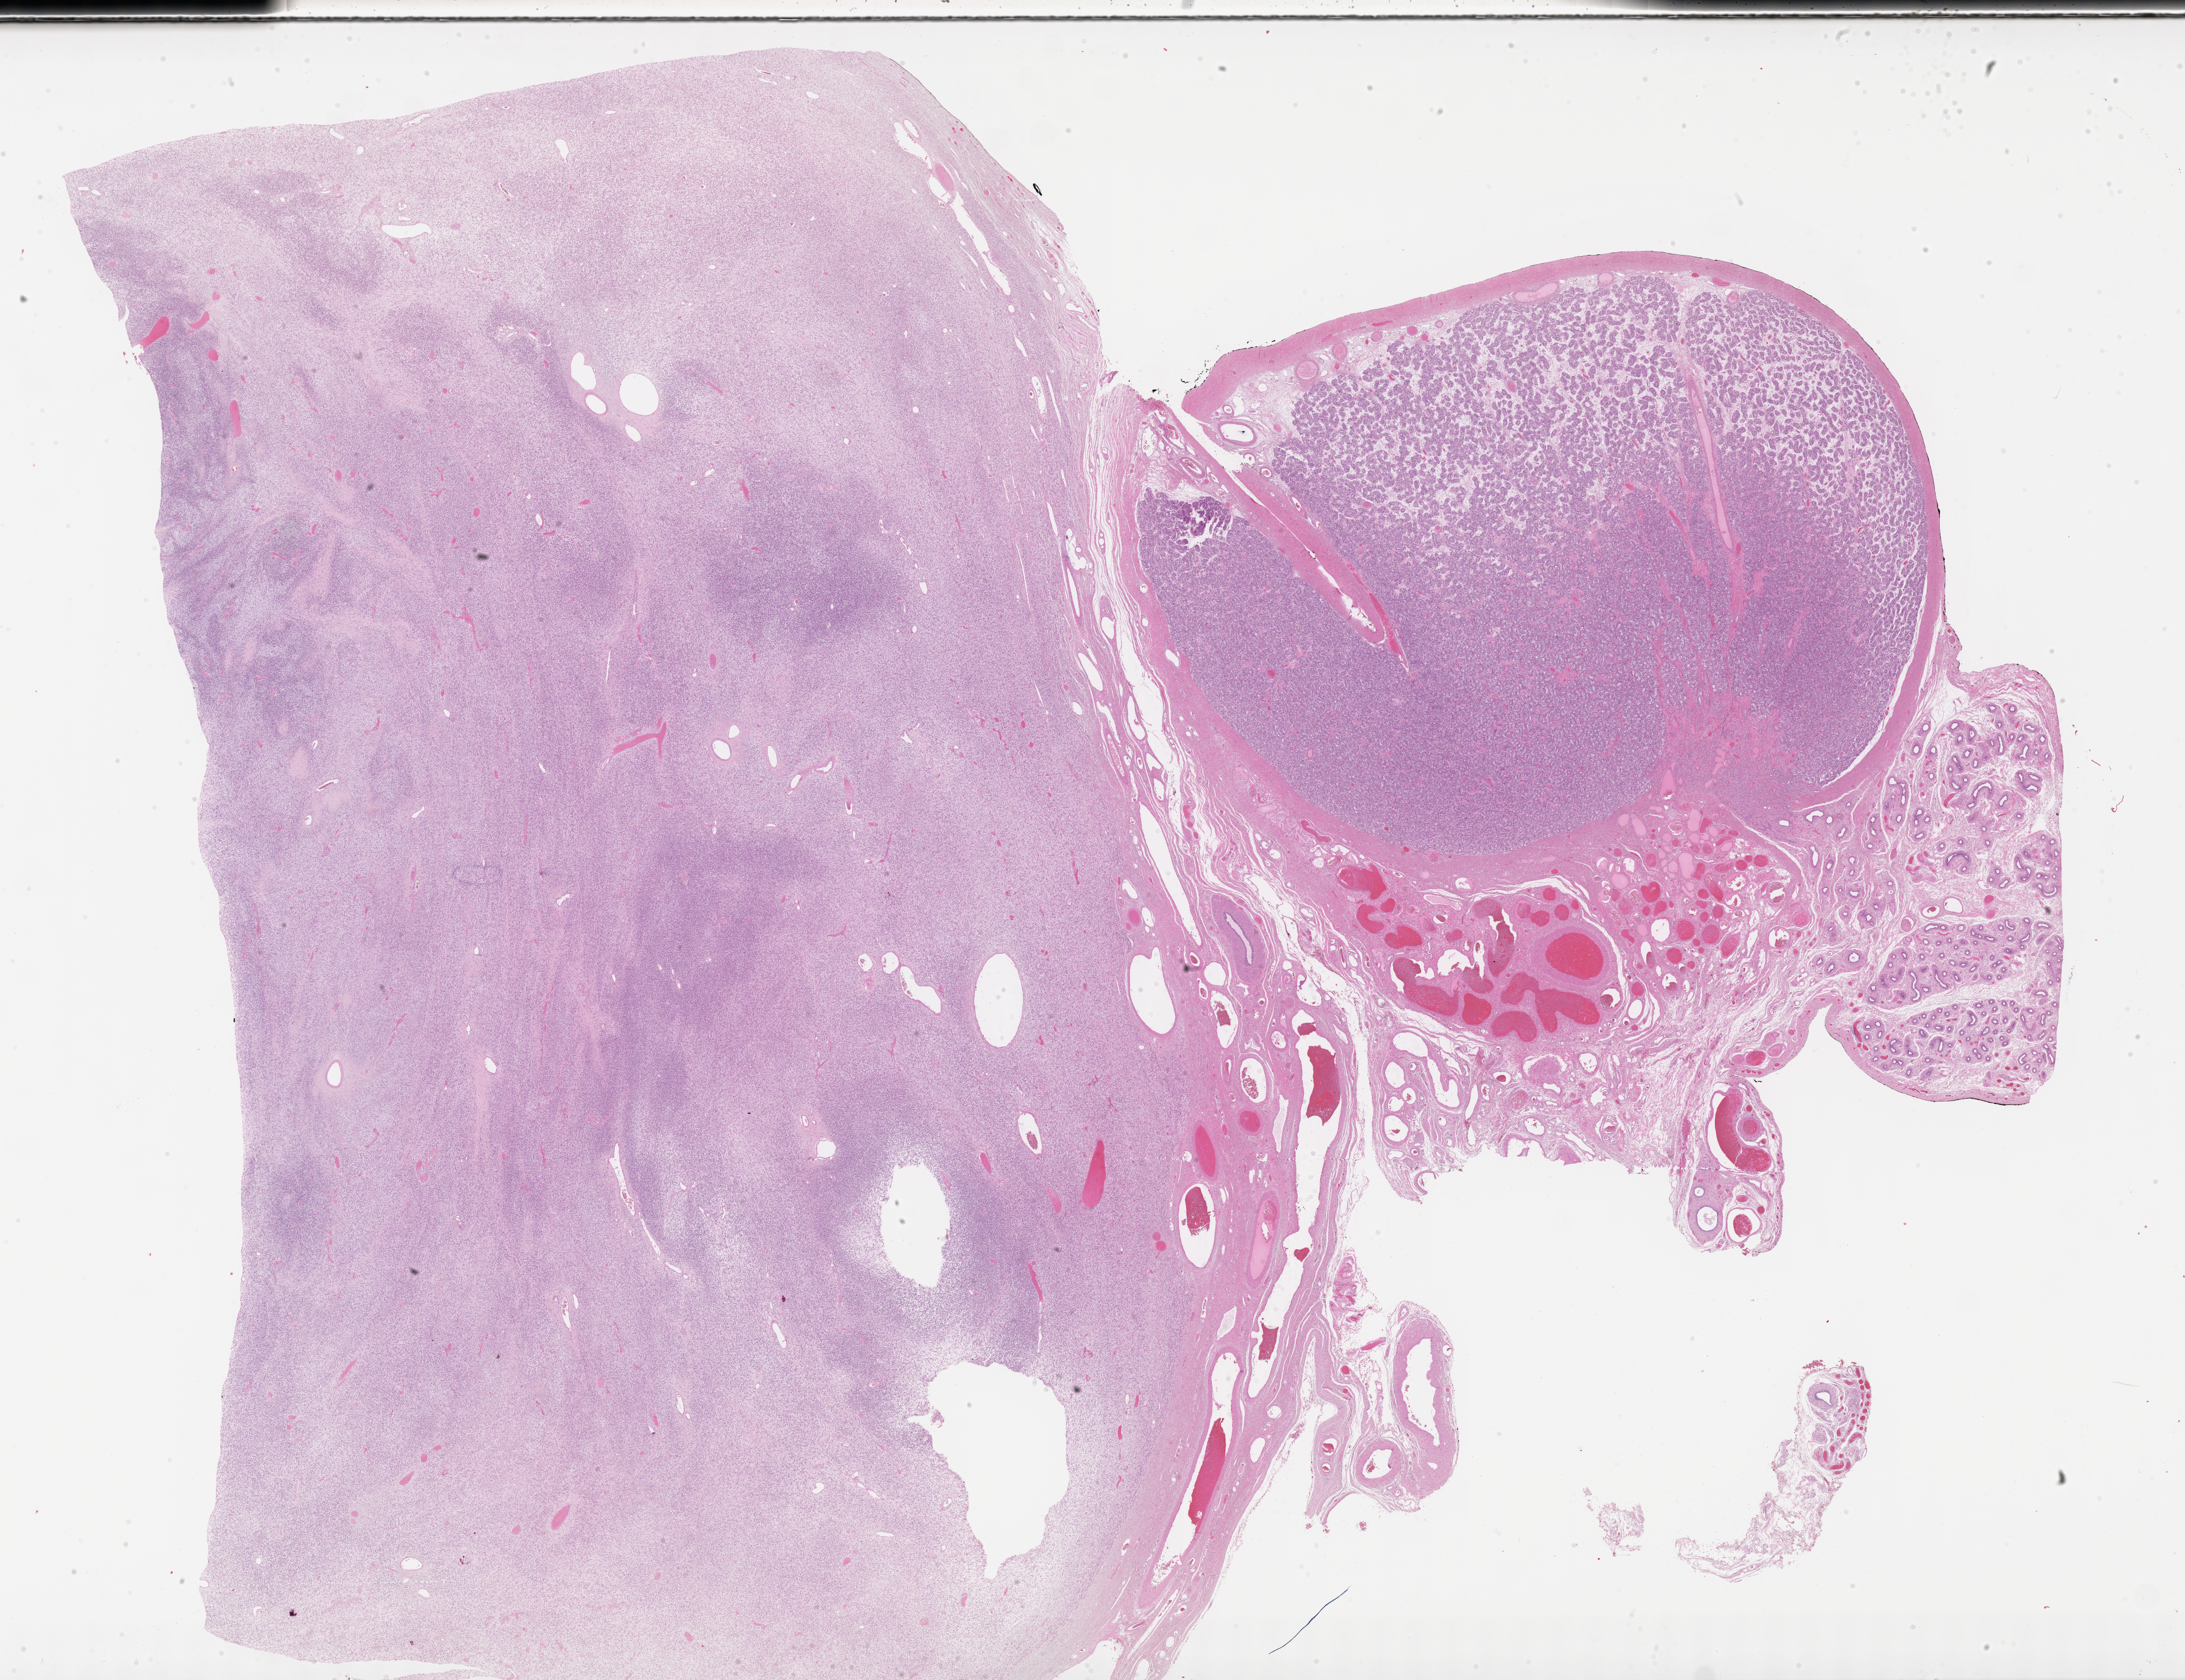
Whole-slide image, hematoxylin and eosin (H&E) stain of tumor tissue, low-resolution overview of the scanned area, about 30.7 x 23.6 mm, formalin-fixed paraffin-embedded section, sample anatomic site: paratesticular, left. Patient: male, age 4.8 years at diagnosis.
Diagnosis: rhabdomyosarcoma; histological classification: embryonal rhabdomyosarcoma.